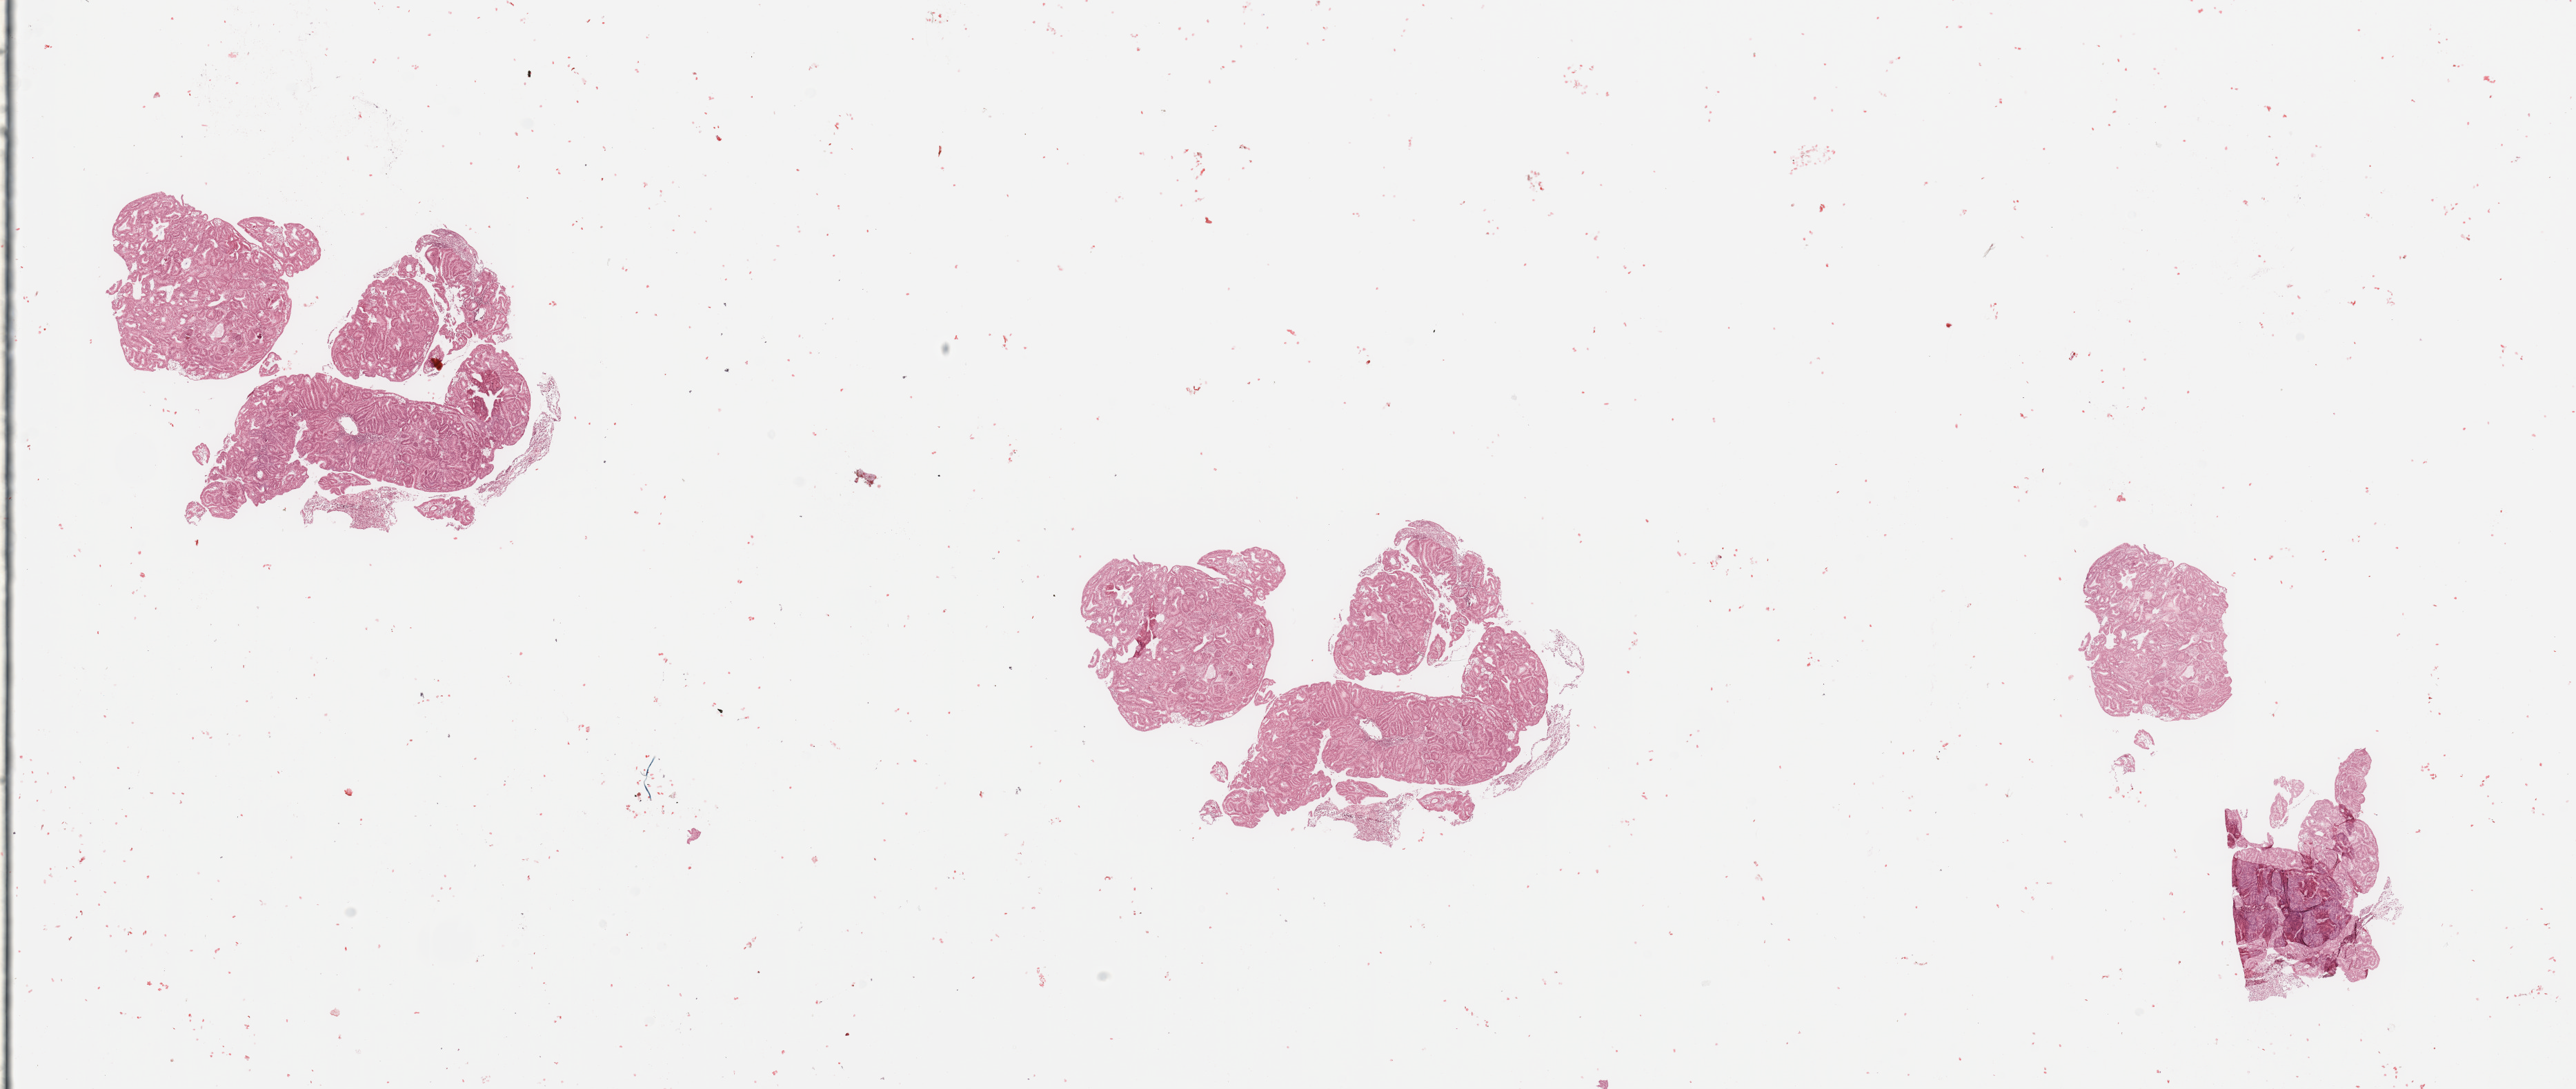
Digitized H&E tissue section (whole slide), a low-resolution overview of the entire scanned area, about 29.5 x 12.5 mm (from a 20x scan); tumour tissue sample, sampled site: uterus. Patient: female, age 68 years. Composition of this section per pathologist review: tumour nuclei 90%, necrosis 0%.
Histologic diagnosis: Endometrioid adenocarcinoma, NOS.